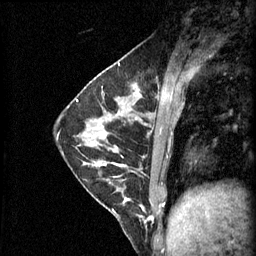
Breast MRI (dynamic contrast-enhanced), one sagittal slice; slice 19 of 60 in the series (ordered by position); 3 images stored at this slice position (order not interpretable as contrast timing); 1.5 T; TE 4.2 ms, TR 11 ms; 2.1 mm slice thickness; 256 × 256 image matrix, field of view 180 × 180 mm. Patient: female, 29 years.
Annotated regions visible in this slice (semi-automatic segmentation, software-assisted and operator-edited):
- analysis volume of interest (the breast-tissue region the enhancement analysis was run in; not a lesion): bounding box <93,164,153,229> (left, top, right, bottom; pixels)
- tumour enhancement mask (voxels above the 70 % enhancement threshold inside the analysis volume of interest): <99,164,152,221>